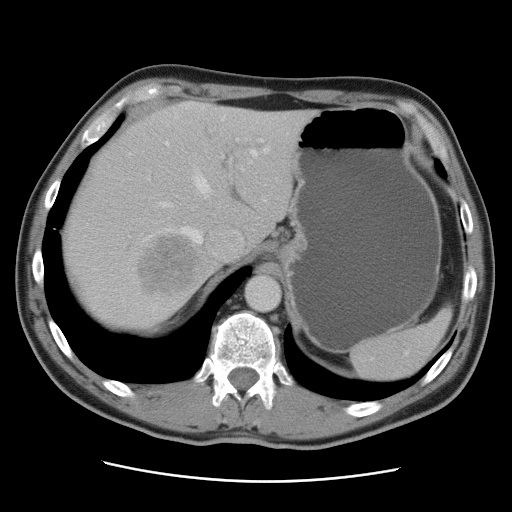
Contrast-enhanced abdominal CT, one axial slice; slice 69 of 89 in the series (ordered by position); 120 kVp; intravenous contrast given; soft-tissue window (W 400 / L 40 HU); 512 × 512 image matrix, field of view 366 × 366 mm. Male patient, age 59 years. From the clinical record (not read from this slice): diagnosis: colorectal cancer liver metastases, imaged before liver resection; multiple liver metastases: yes; largest metastasis: 0.6 cm; disease in both lobes: yes.
Structures marked on this image (expert manual segmentation):
- hepatic veins: bounding box (x1, y1, x2, y2) in pixels: (129, 117, 269, 255)
- liver: (61, 101, 313, 333)
- planned liver remnant (the part of the liver to remain after resection): (109, 102, 313, 245)
- portal vein (with intrahepatic branches): (148, 139, 263, 179)
- liver metastasis: (140, 237, 200, 293)